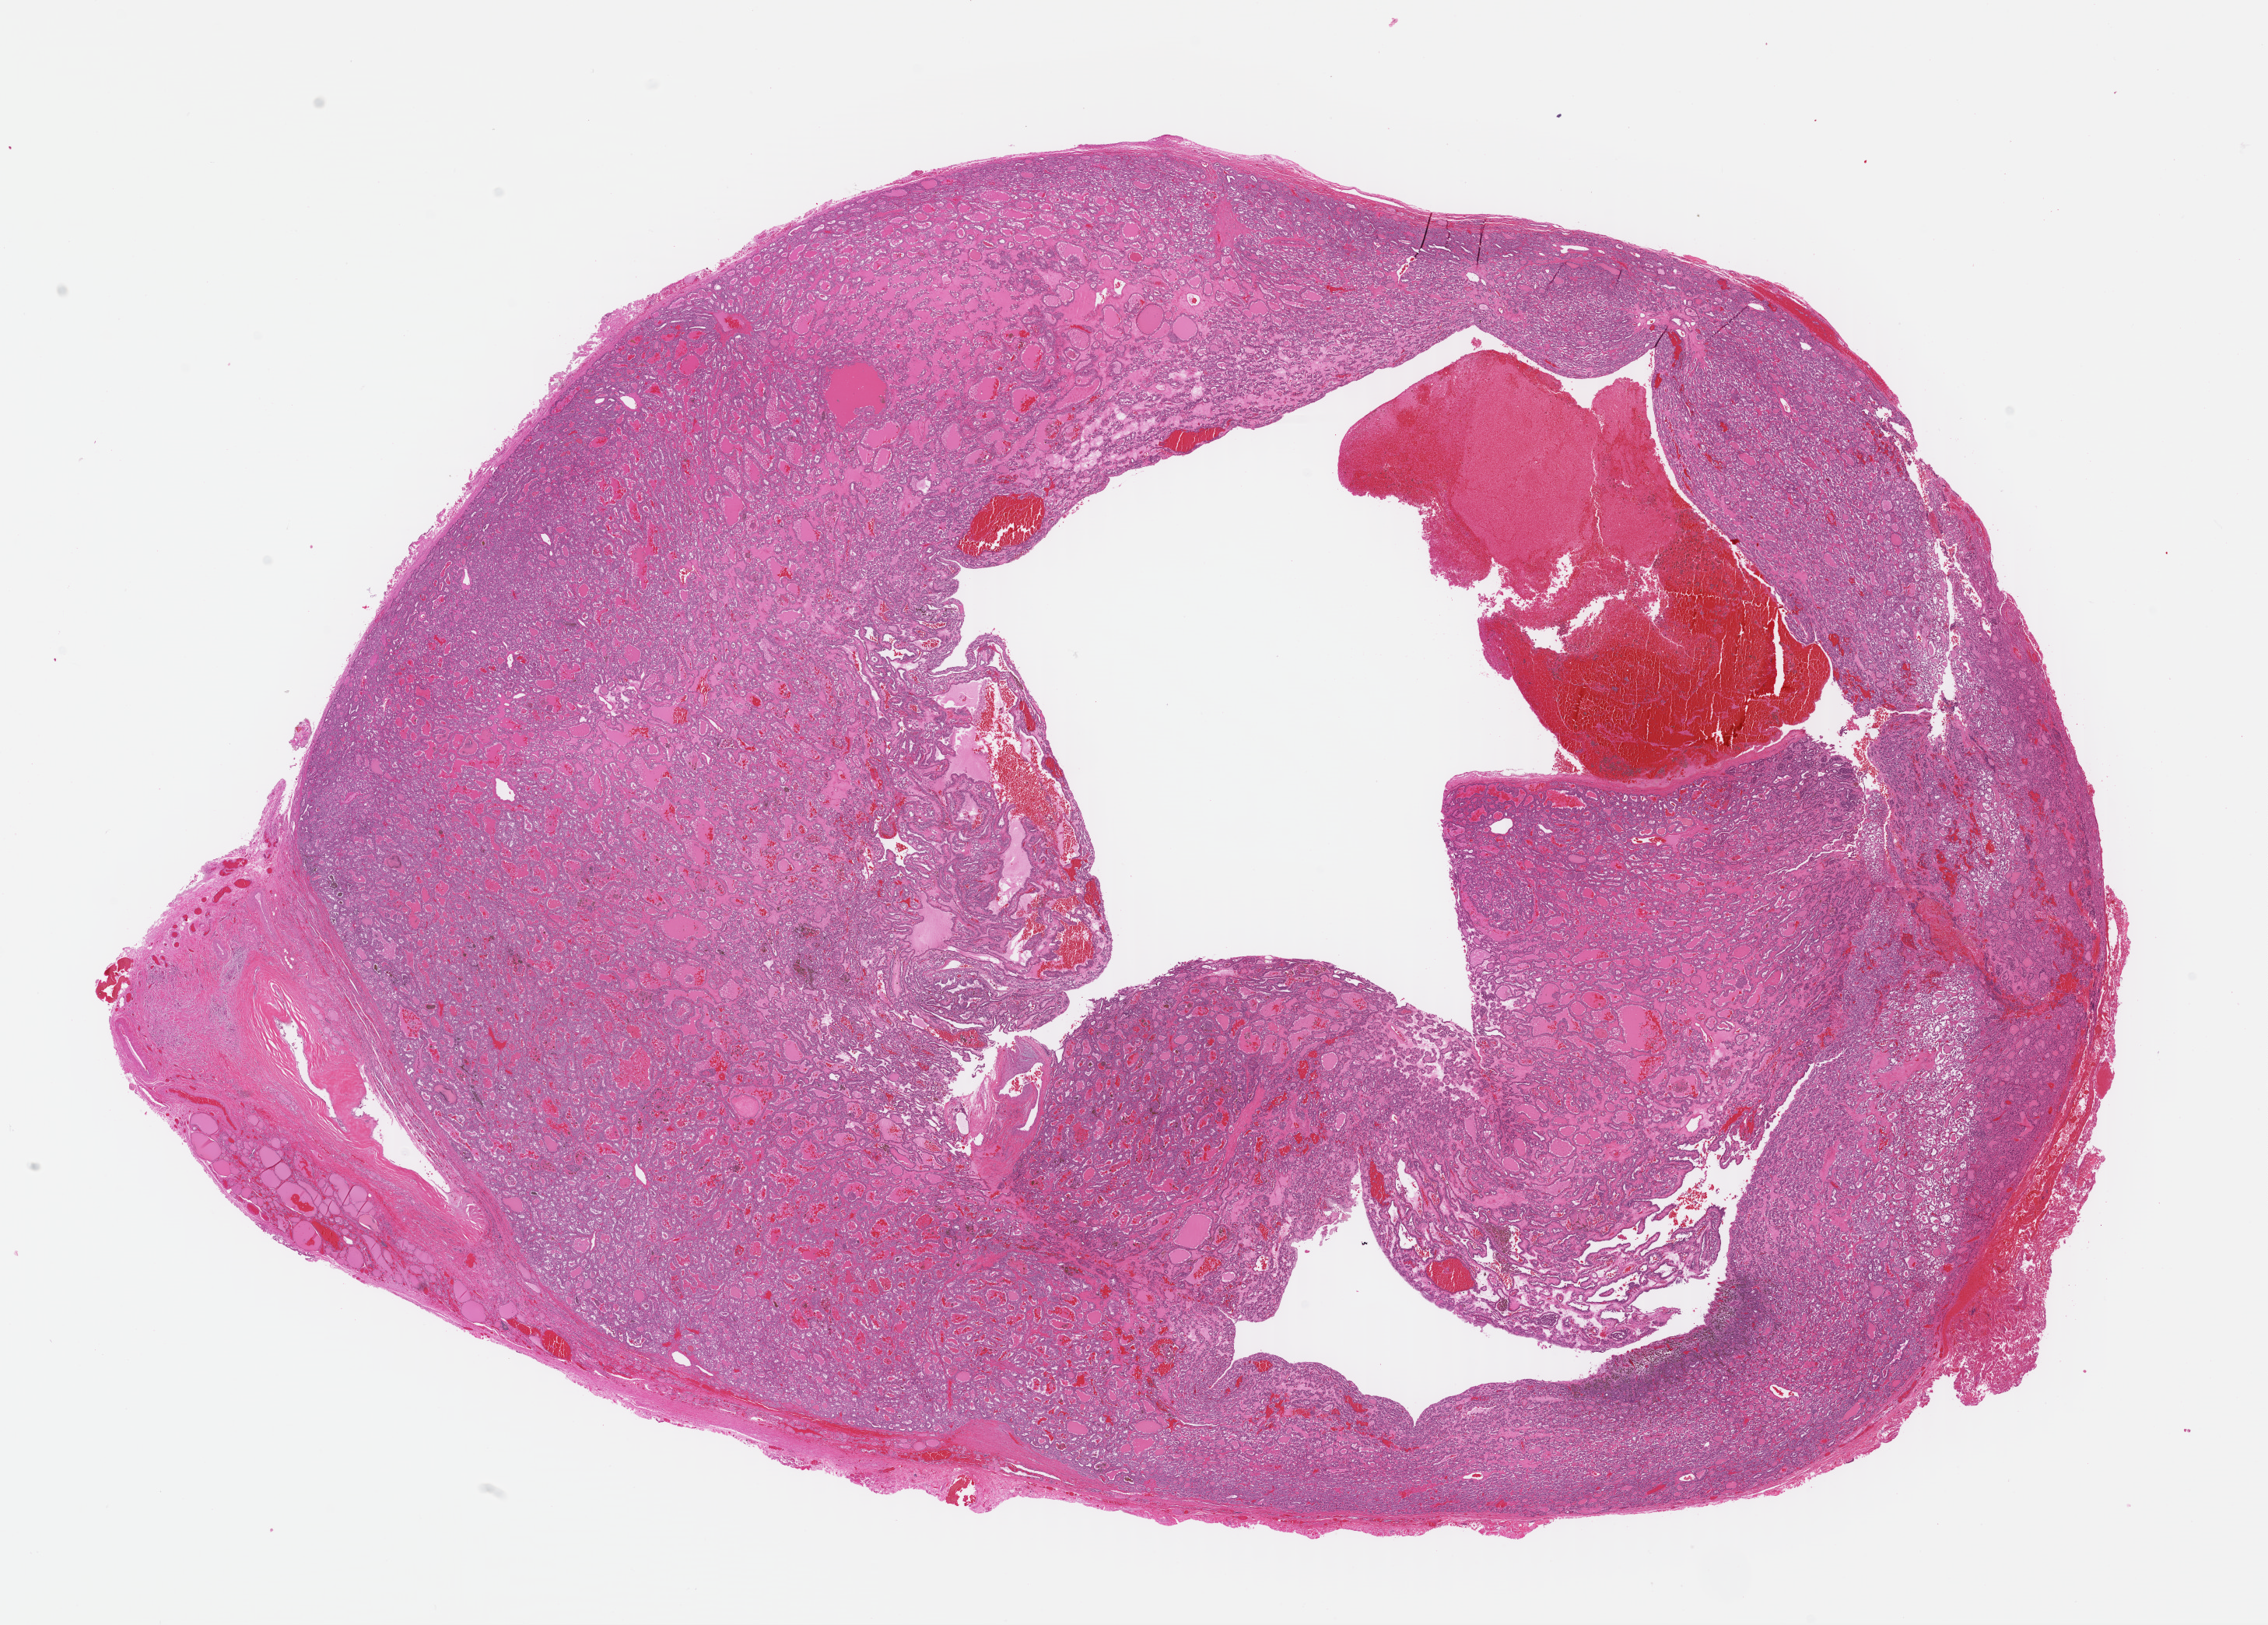
Whole-slide histology image, H&E, a low-resolution overview of the entire scanned area, about 22.9 x 16.4 mm (acquisition: 40x scan), FFPE section, thyroid, primary tumour sample. Patient: female, age at initial diagnosis 36 years.
Histologic diagnosis: Papillary adenocarcinoma, NOS.